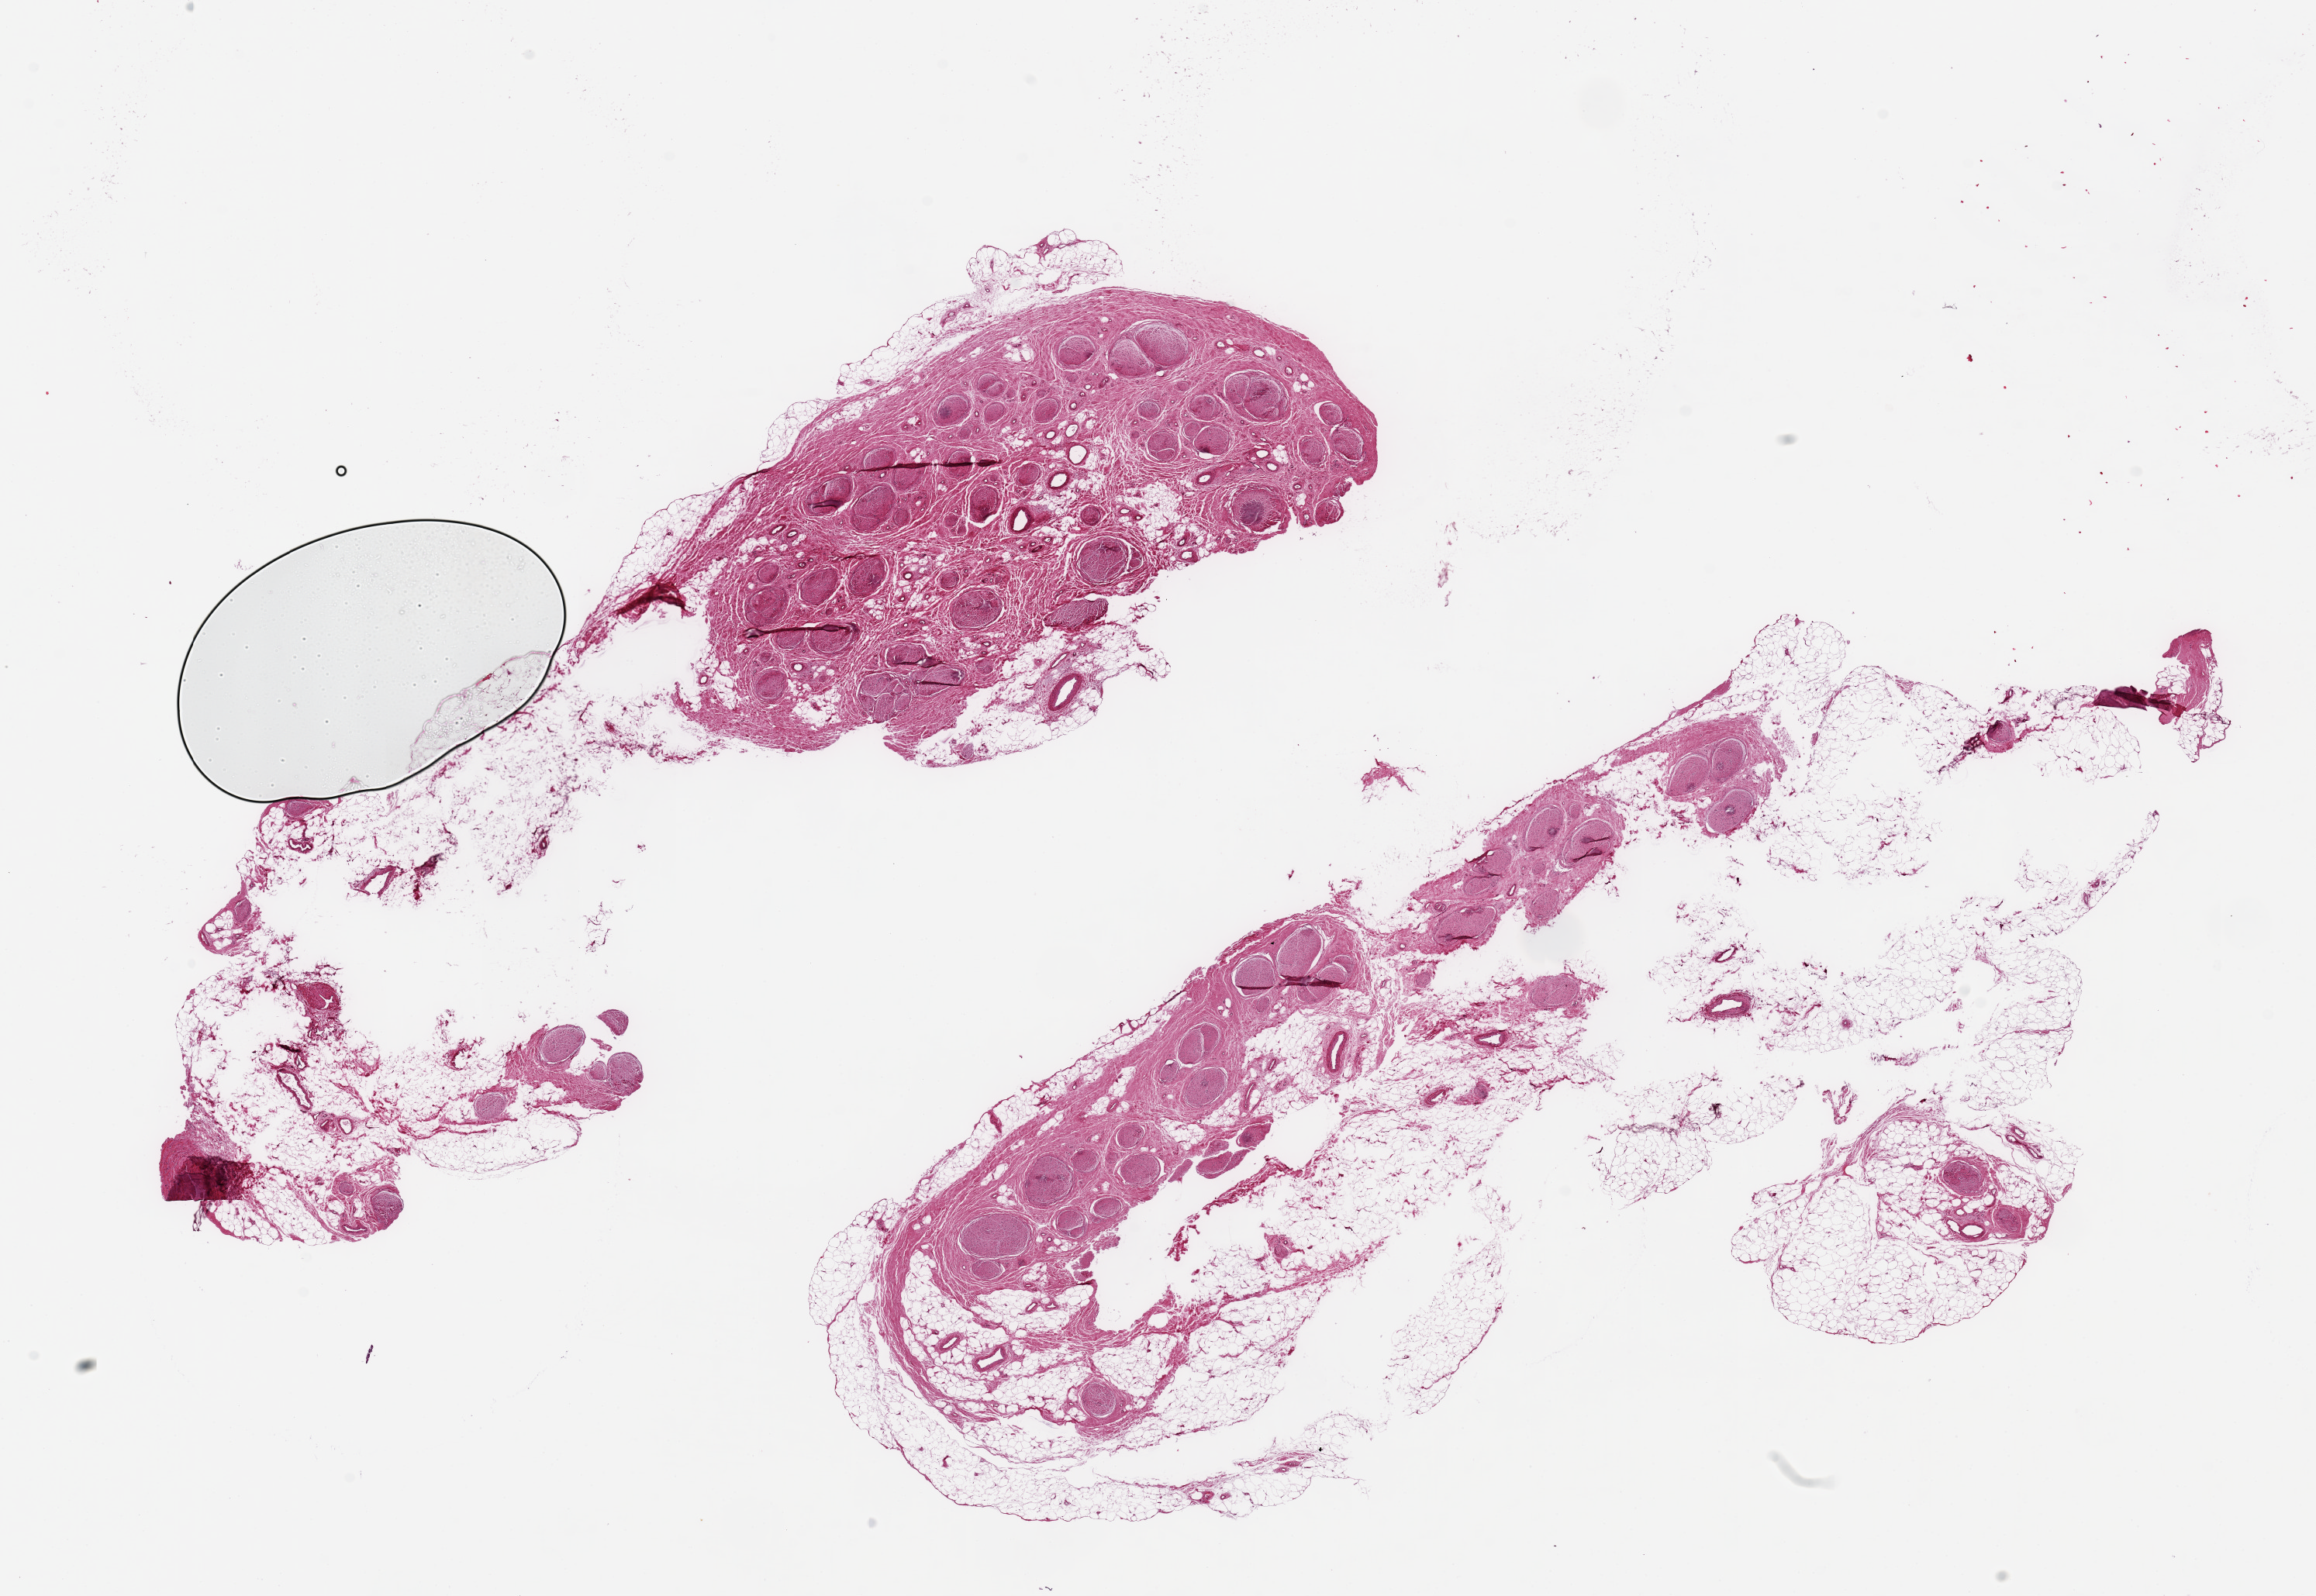
Whole-slide image, hematoxylin and eosin (H&E) stain — shown as a low-resolution overview of the whole scanned area (about 23.6 x 16.3 mm); PAXgene-fixed, paraffin-embedded tissue; section of tibial nerve (target tissue); tissue donor sample. Donor sex: male.
Pathologist's review note for this sample: 2 pieces, one 7x3mm, one 10x1mm, both with extensive adherent fat.